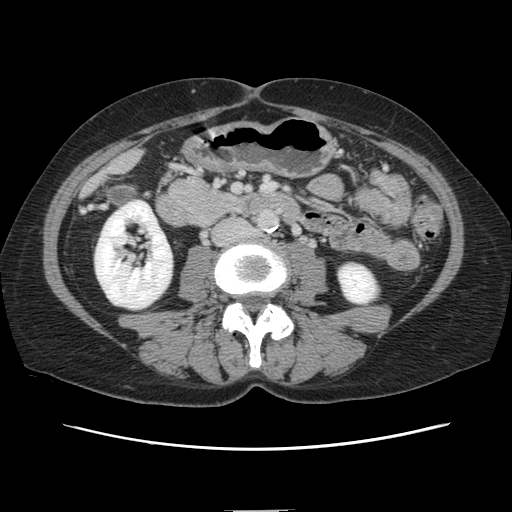
Contrast-enhanced abdominal CT, one axial slice. Slice 25 of 141 in the series (ordered by position). Intravenous contrast given. Soft-tissue window (W 400 / L 40 HU). 2.5 mm slice thickness. 512 × 512 image matrix, field of view 350 × 350 mm. Female patient, age 63 years. From the clinical record (not read from this slice): diagnosis: colorectal cancer liver metastases, imaged before liver resection.
Structures marked on this image (outlined manually by an expert reader):
- liver: bounding box <87,153,139,192> (left, top, right, bottom; pixels)